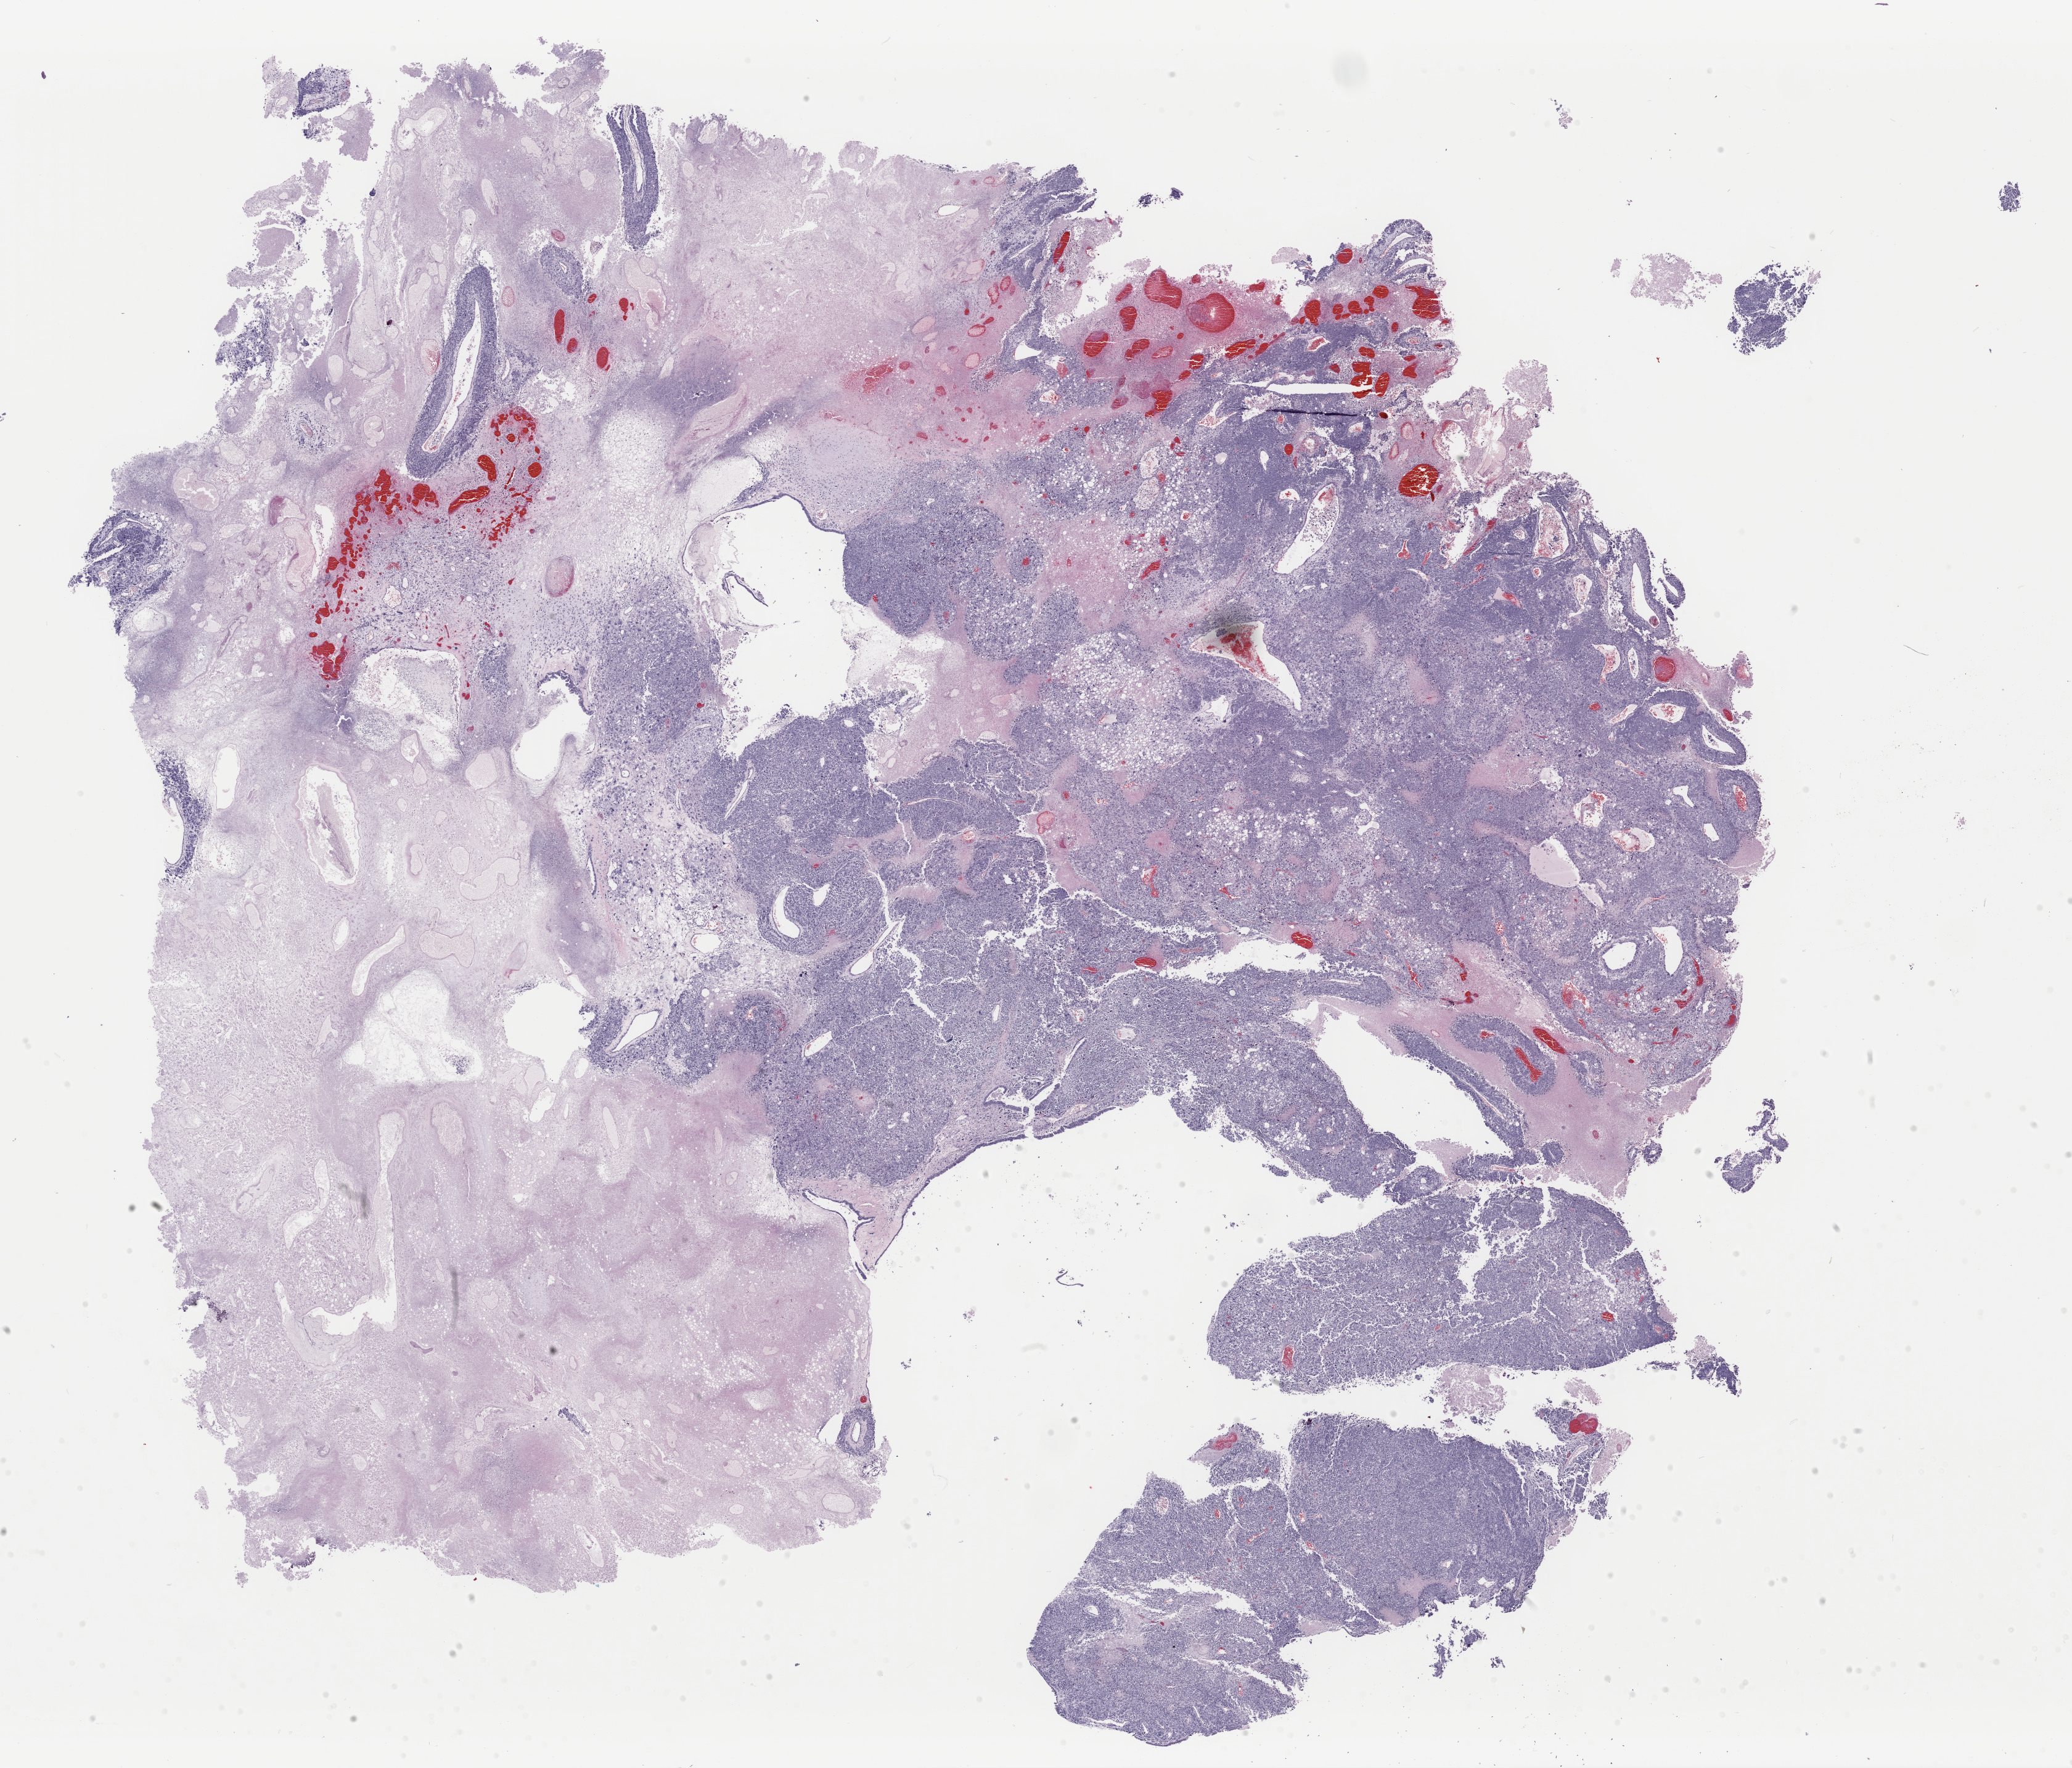
Digitized Hematoxylin and eosin (H&E) stained tissue section (whole slide), whole scanned area (about 26.5 x 22.7 mm) shown as a low-resolution overview, FFPE section, sample: primary tumour, uterus. Female patient; age at initial diagnosis 69 years.
Diagnosis: Mullerian mixed tumor. FIGO stage: IVB.